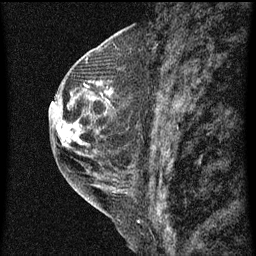
Breast MRI (dynamic contrast-enhanced), one sagittal slice; position 23 of 60 along the scan axis; dynamic contrast-enhanced series, image 2 of 3 at this slice position (ordered by acquisition); 1.5 T; TE 4.2 ms, TR 8 ms; 2 mm slice thickness; 256 × 256 image matrix, field of view 180 × 180 mm. Patient: female, 48 years.
Annotated regions visible in this slice (semi-automatically segmented with operator editing):
- analysis volume of interest (the breast-tissue region the enhancement analysis was run in; not a lesion): bounding box (x1, y1, x2, y2) in pixels: (89, 72, 114, 113)
- tumour enhancement mask (voxels above the 70 % enhancement threshold inside the analysis volume of interest): (99, 82, 114, 103)